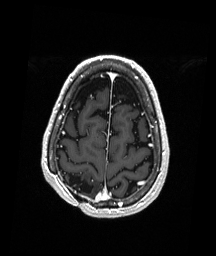
Brain MRI from a brain-tumour surgery series, one axial slice; slice 52 of 192 in the series (ordered by position); T1-weighted post-contrast; 216 × 256 image matrix, field of view 211 × 250 mm. From the clinical record (not read from this slice): histopathology: Astrocytoma; WHO grade: 3; IDH mutation: yes; tumour location: Right Parietal.
Annotated regions visible in this slice (outlined manually by an expert reader):
- previous resection cavity: bounding box (x1, y1, x2, y2) in pixels: (63, 173, 93, 194)